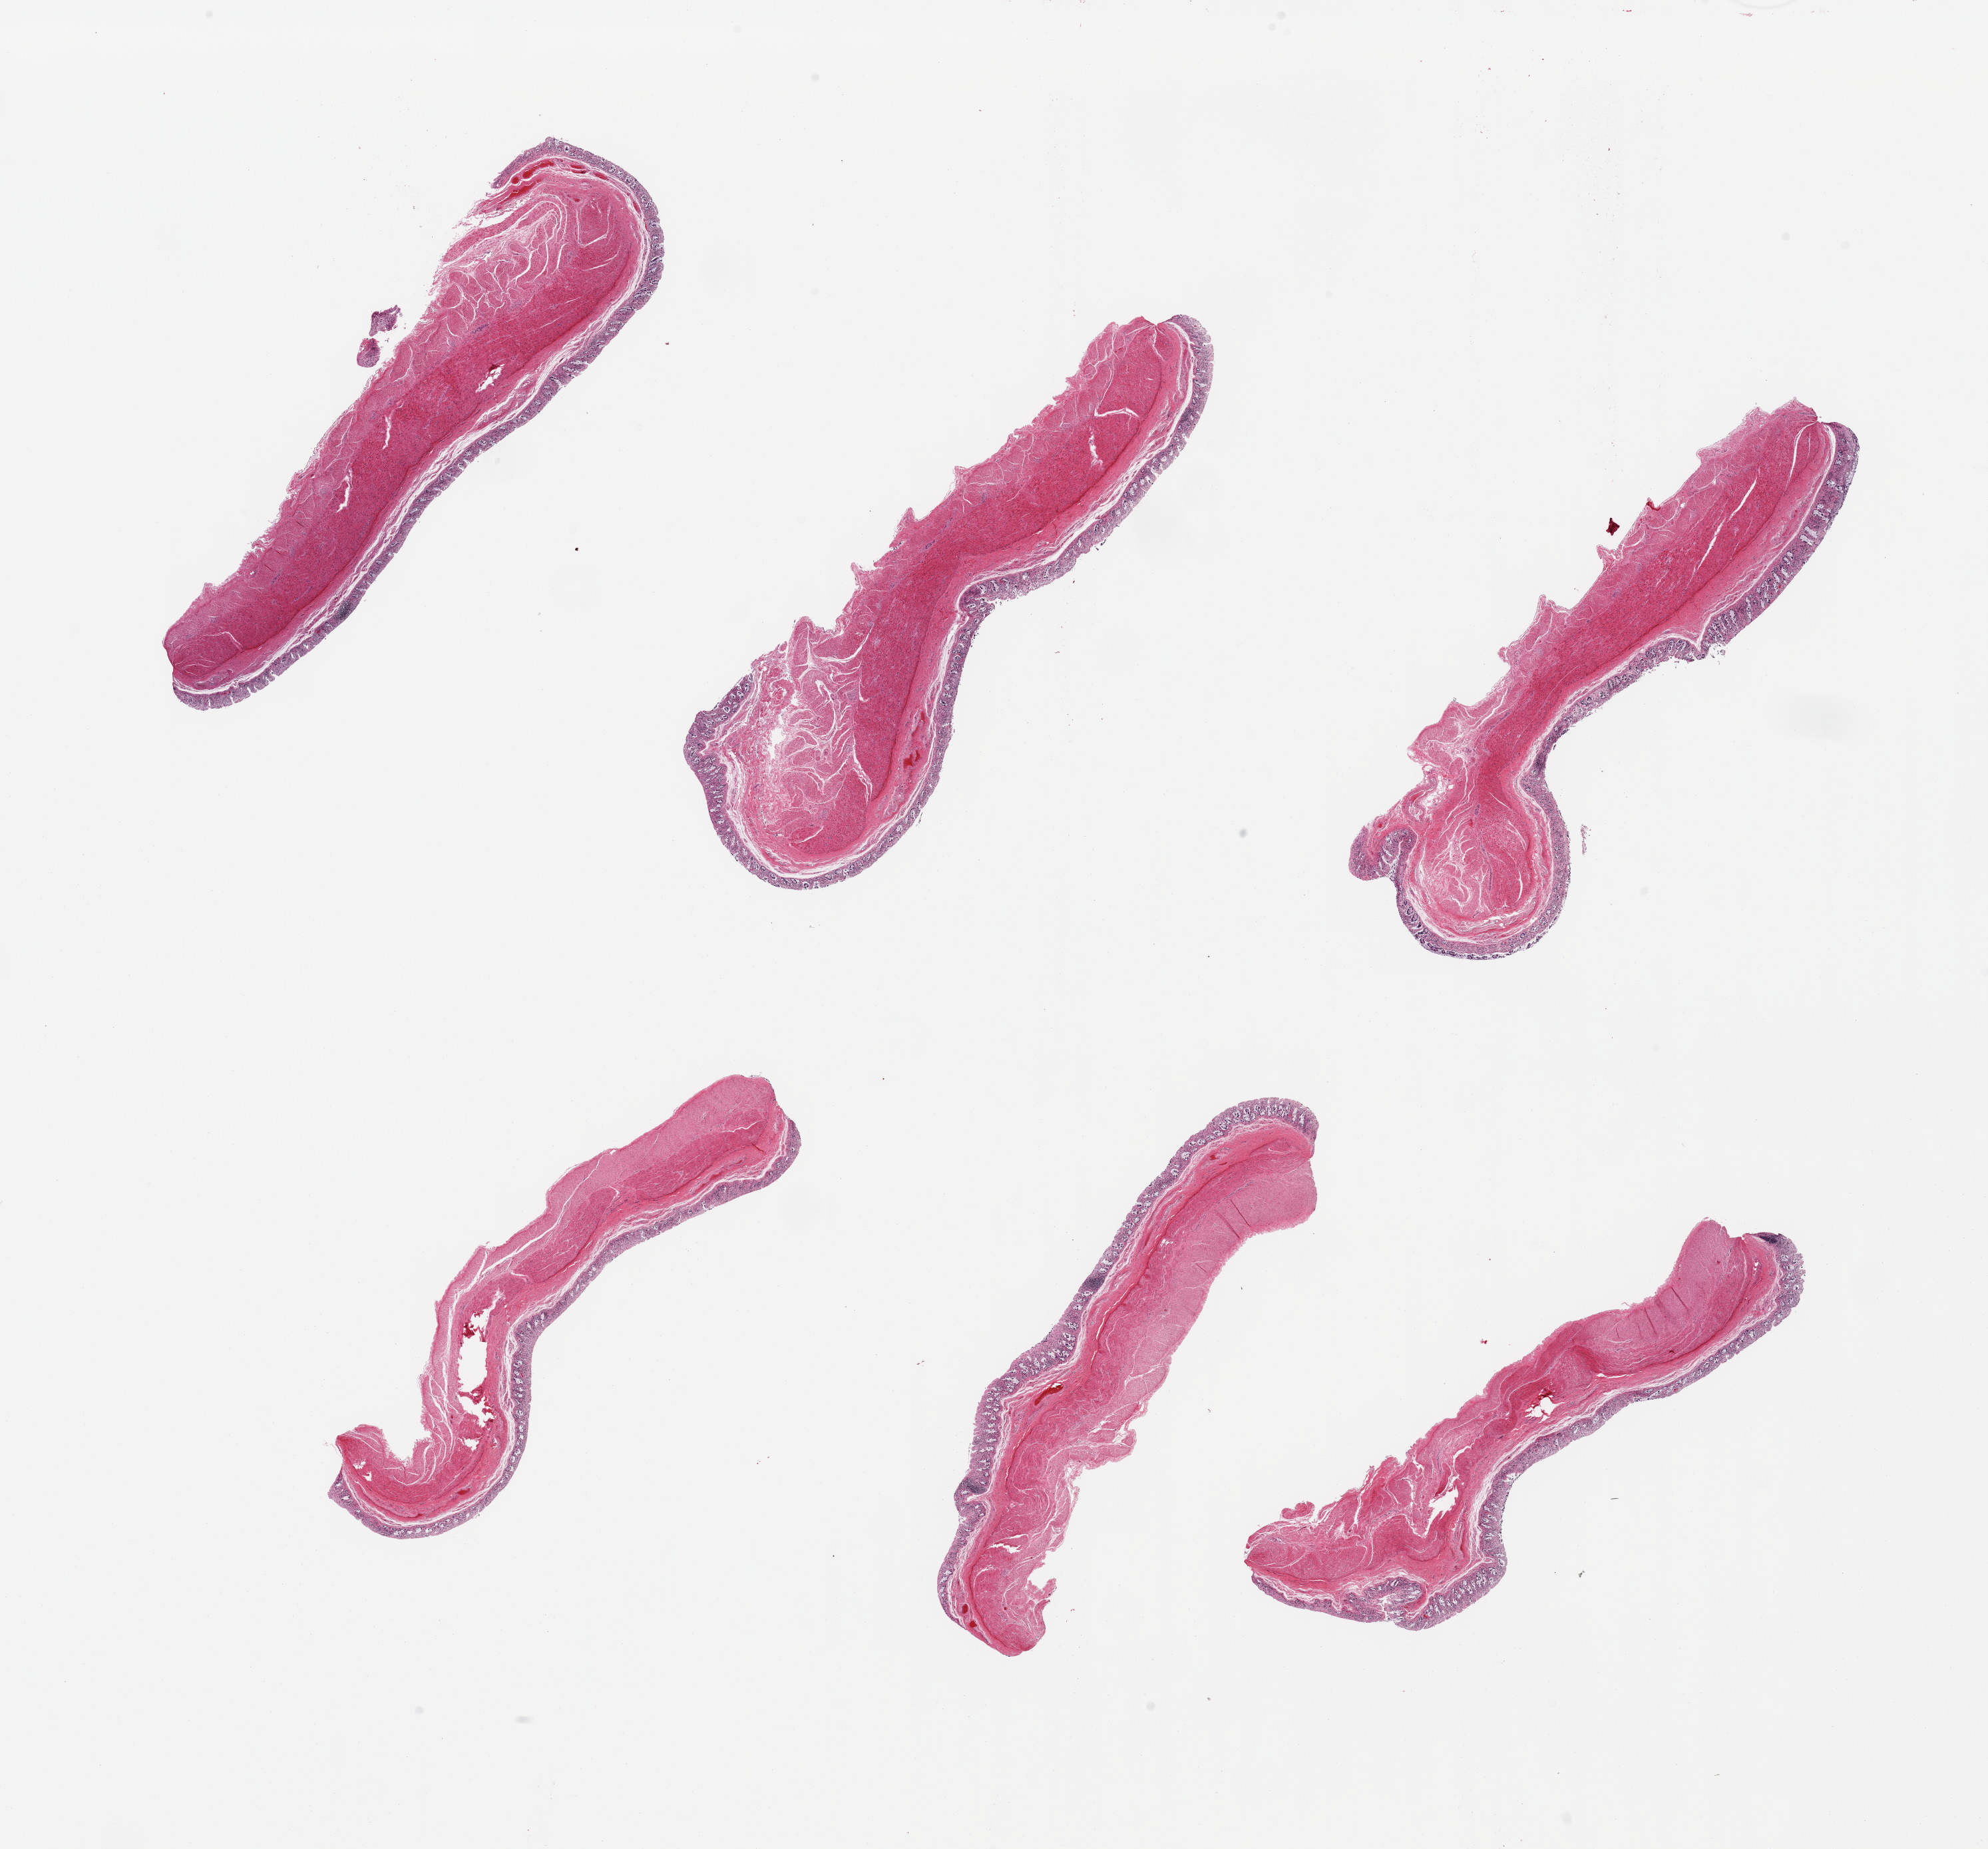
Digitized haematoxylin and eosin-stained section, brightfield, a low-resolution overview of the entire scanned area, about 23.6 x 22.0 mm; PAXgene-fixed, paraffin-embedded tissue; section of transverse colon (target tissue); donor tissue sample. Donor: female.
• pathologist's review note for this sample: 6 pieces, mucosa is up to ~0.25mm but glandulare elements completely autolyzed